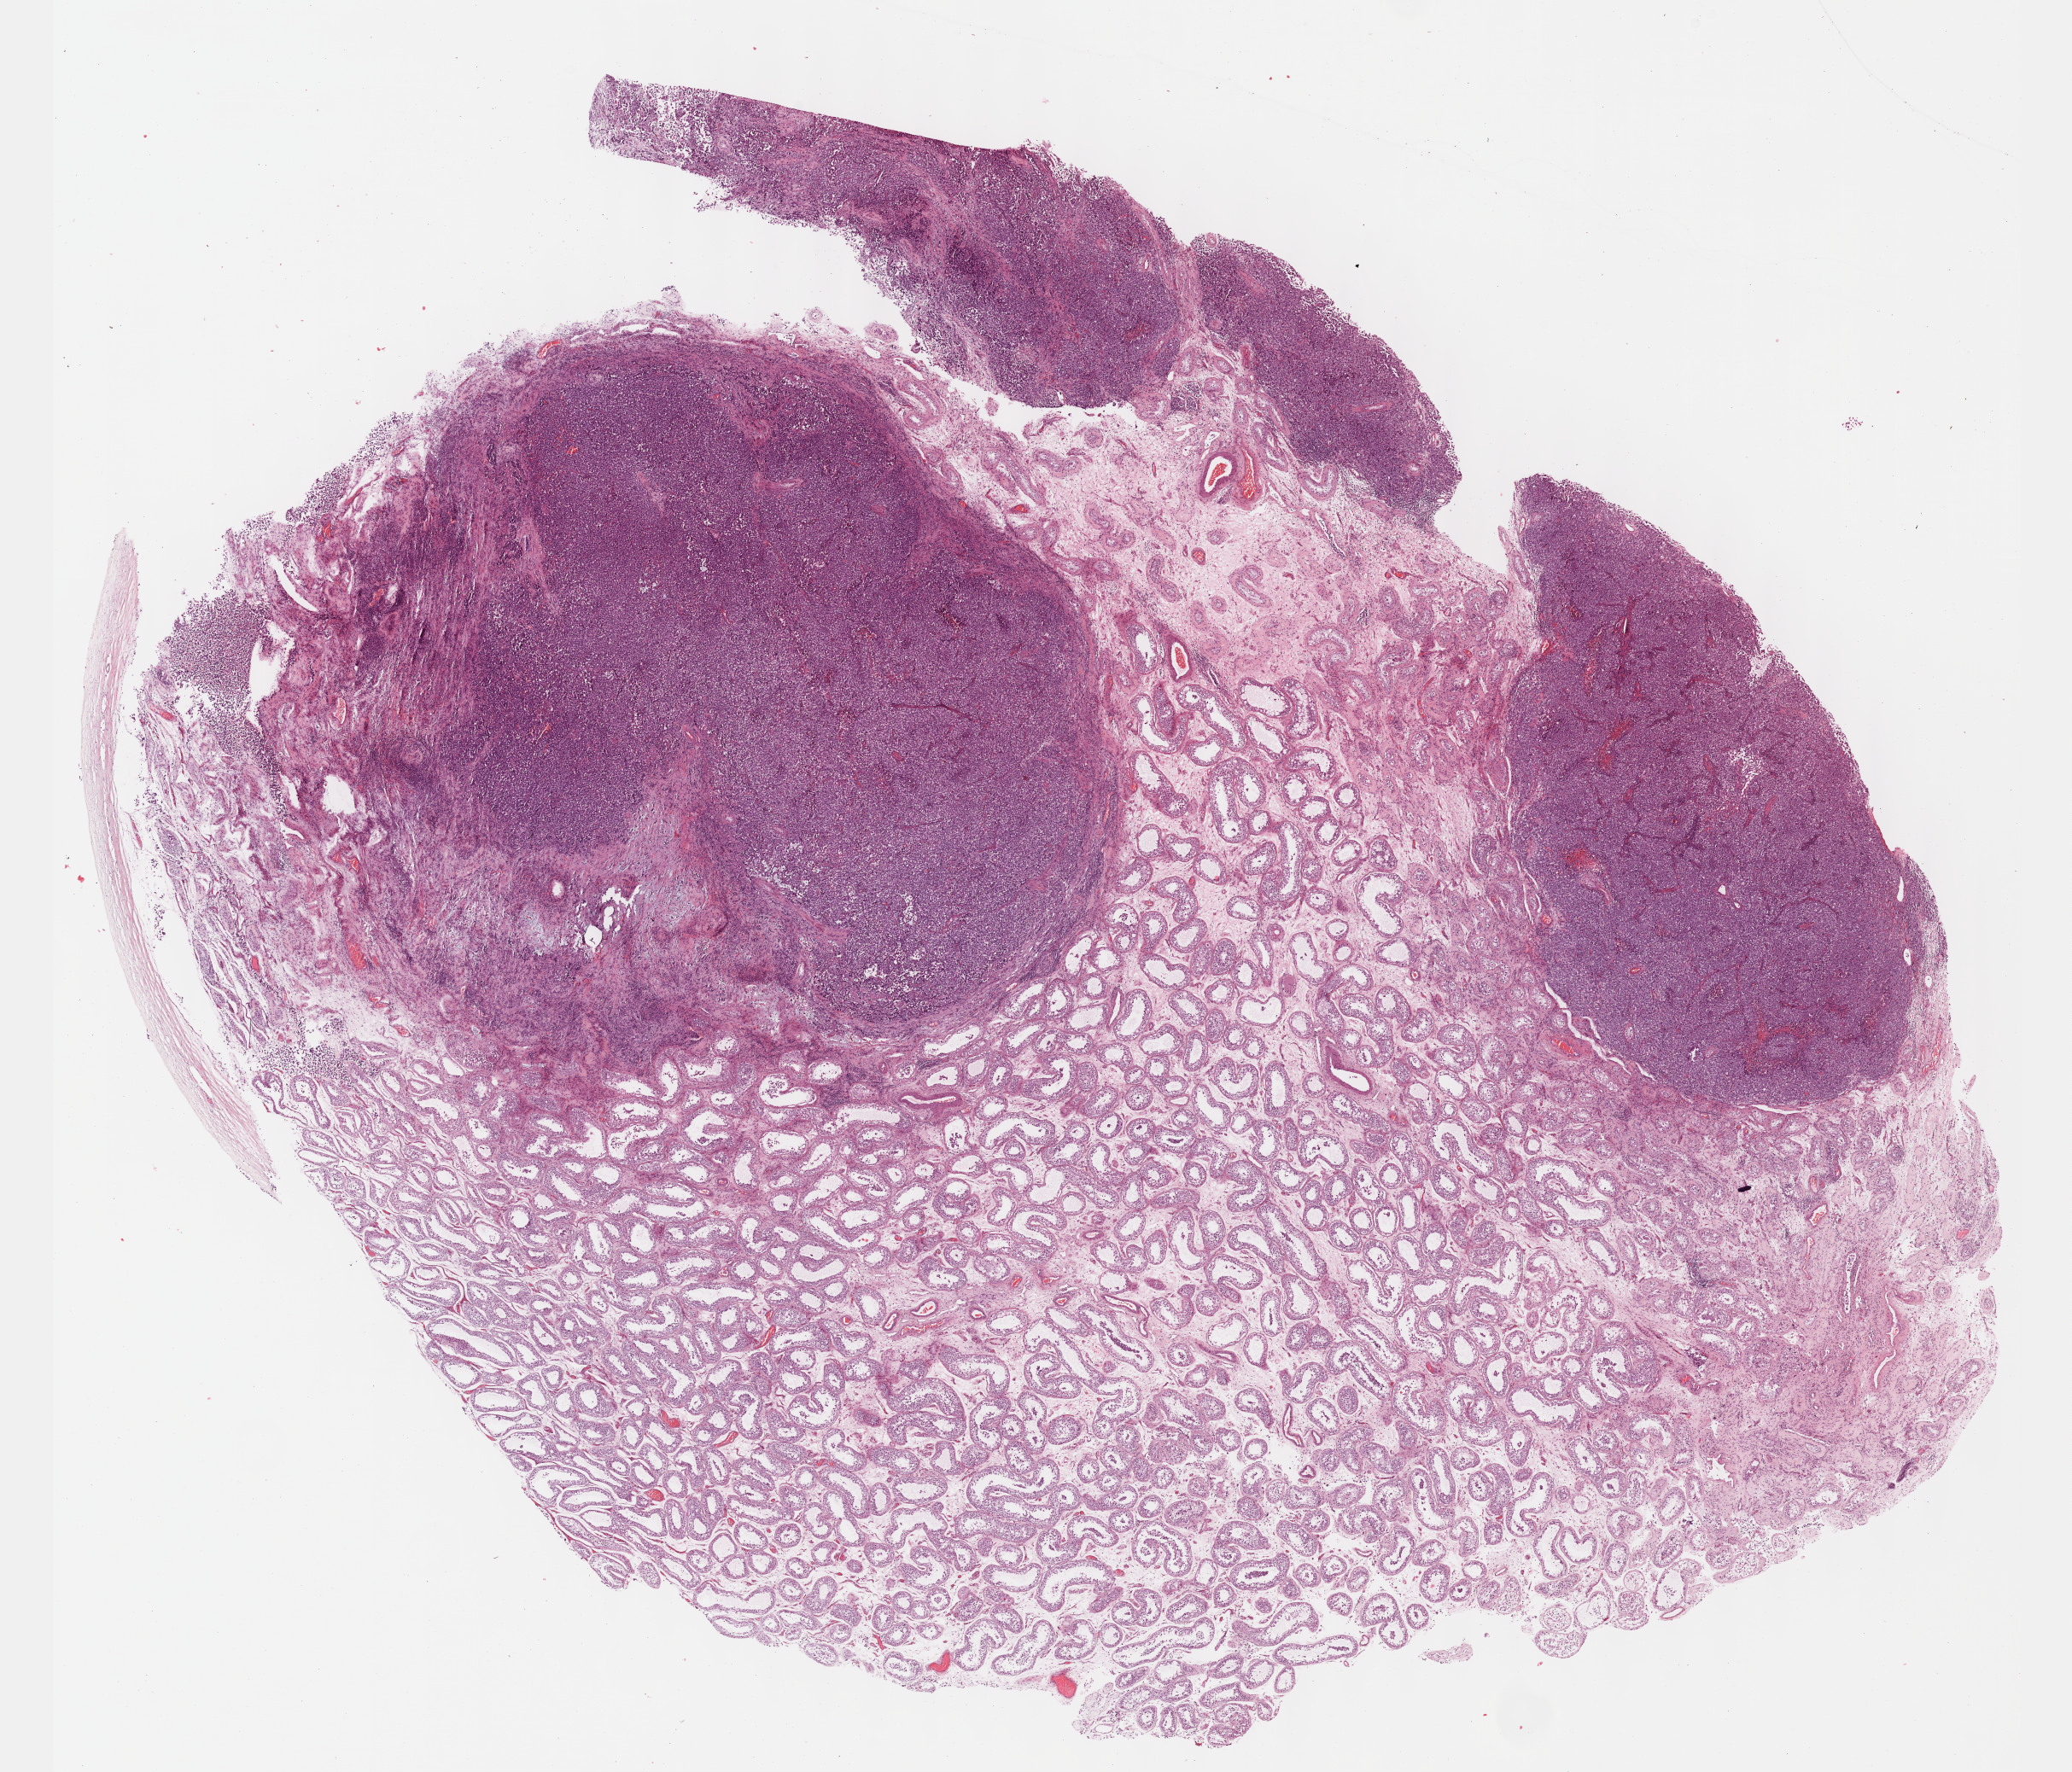
Digitized H&E tissue section (whole slide), shown as a low-resolution overview of the whole scanned area (about 19.6 x 16.8 mm, from a 40x scan), formalin-fixed paraffin-embedded (FFPE) diagnostic section, primary tumour sample from the testis. Patient: male, age at initial diagnosis 44 years.
Histologic diagnosis: Seminoma, NOS. TNM: T2 NX M0. AJCC pathologic stage: IB (7th edition). Laterality: right.